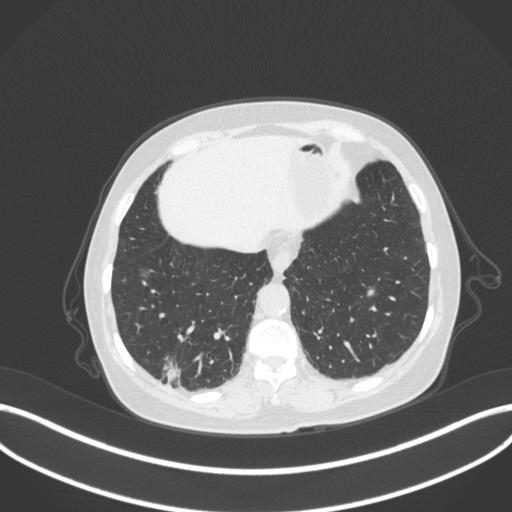
Chest CT, one axial slice; reconstruction kernel B31f; 120 kVp; lung window (W 1500 / L -600 HU); 512 × 512 image matrix, field of view 400 × 400 mm. Female patient, age 69 years. From the clinical record (not read from this slice): clinical TNM (as recorded): T1b N0 M0; histopathological grade: G2-3.
Structures marked on this image (rectangle marked by the reading radiologist):
- lung tumour (recorded histology: adenocarcinoma): bounding box (x1, y1, x2, y2) in pixels: (158, 353, 184, 386)